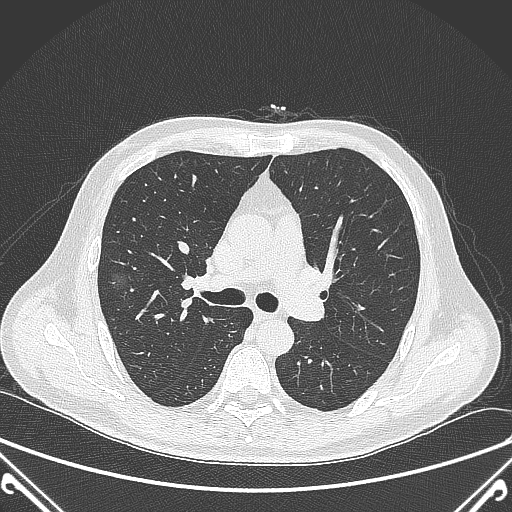
Chest CT, one axial slice; slice 230 of 360 in the series (ordered by position); 120 kVp; lung window (W 1500 / L -600 HU); 1 mm slice thickness; 512 × 512 image matrix. Male patient, age 64 years. From the clinical record (not read from this slice): clinical TNM (as recorded): T1c N0 M0.
Structures marked on this image (bounding box drawn by a radiologist):
- lung tumour (recorded histology: adenocarcinoma): box from (x=106, y=265) to (x=126, y=298) px